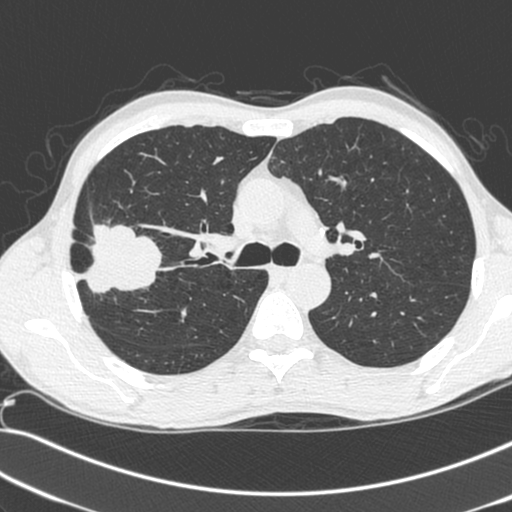
Low-dose screening chest CT, axial slice; baseline screening round; lung window (W 1500 / L -600 HU). Male, age 55 years at enrolment.
Lesion marked by an expert reader, box from (x=69, y=226) to (x=154, y=301) px. Screening reader's record for this exam (one nodule recorded; not confirmed to be the boxed lesion): non-calcified nodule or mass ≥4 mm, right upper lobe, 52 × 39 mm, spiculated (stellate) margins, soft tissue attenuation. Later outcome: lung cancer diagnosed 25 days after this screen — large cell neuroendocrine carcinoma, right upper lobe, poorly differentiated (G3), stage IIB (AJCC 6th edition), 49 mm at pathology.